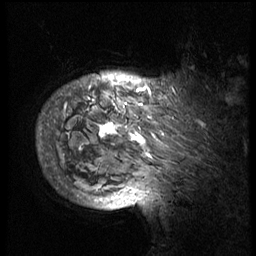
Breast MRI (dynamic contrast-enhanced), one sagittal slice; position 62 of 74 along the scan axis; 3 images stored at this slice position (order not interpretable as contrast timing); 1.5 T; TE 4.2 ms, TR 8.9 ms; 2.5 mm slice thickness; 256 × 256 image matrix, field of view 200 × 200 mm. Female patient, age 57 years. From the clinical record (not read from this slice): setting: breast cancer imaged before/during neoadjuvant chemotherapy; receptor status: HER2-positive.
Structures marked on this image (semi-automatically segmented with operator editing):
- analysis volume of interest (the breast-tissue region the enhancement analysis was run in; not a lesion): bounding box [x1, y1, x2, y2] px = [40, 64, 236, 175]
- tumour enhancement mask (voxels above the 140 % enhancement threshold inside the analysis volume of interest): [41, 81, 203, 158]